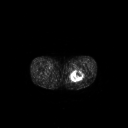
FDG PET of an extremity soft-tissue mass (from a PET/CT study), one axial slice; 128 × 128 image matrix. Male patient, age 44 years. From the clinical record (not read from this slice): histological type: undifferentiated pleomorphic liposarcoma; grade: high; site of the primary tumour: left thigh.
Structures marked on this image (expert contour drawn on MRI and transferred to this co-registered scan by the dataset authors):
- gross tumour volume including surrounding oedema: bounding box <68,70,84,82> (left, top, right, bottom; pixels)
- gross tumour volume (mass): <69,71,82,82>